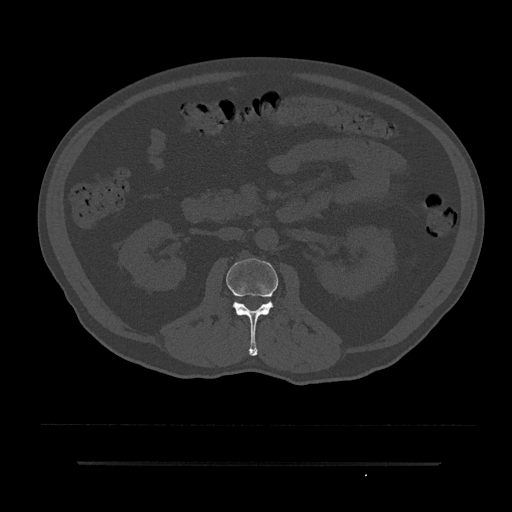
CT including the spine, one axial slice. Position 69 of 797 along the scan axis. Reconstruction kernel Br40s/3. 120 kVp. Bone window (W 1800 / L 400 HU). 512 × 512 image matrix. Patient: male, 59 years. Case-level facts recorded for this patient, not image findings: primary cancer: bile ducts.
Outlined on this slice (semi-automatic segmentation, software-assisted and operator-edited):
- L2 vertebra: bounding box [x1, y1, x2, y2] px = [226, 258, 285, 356]